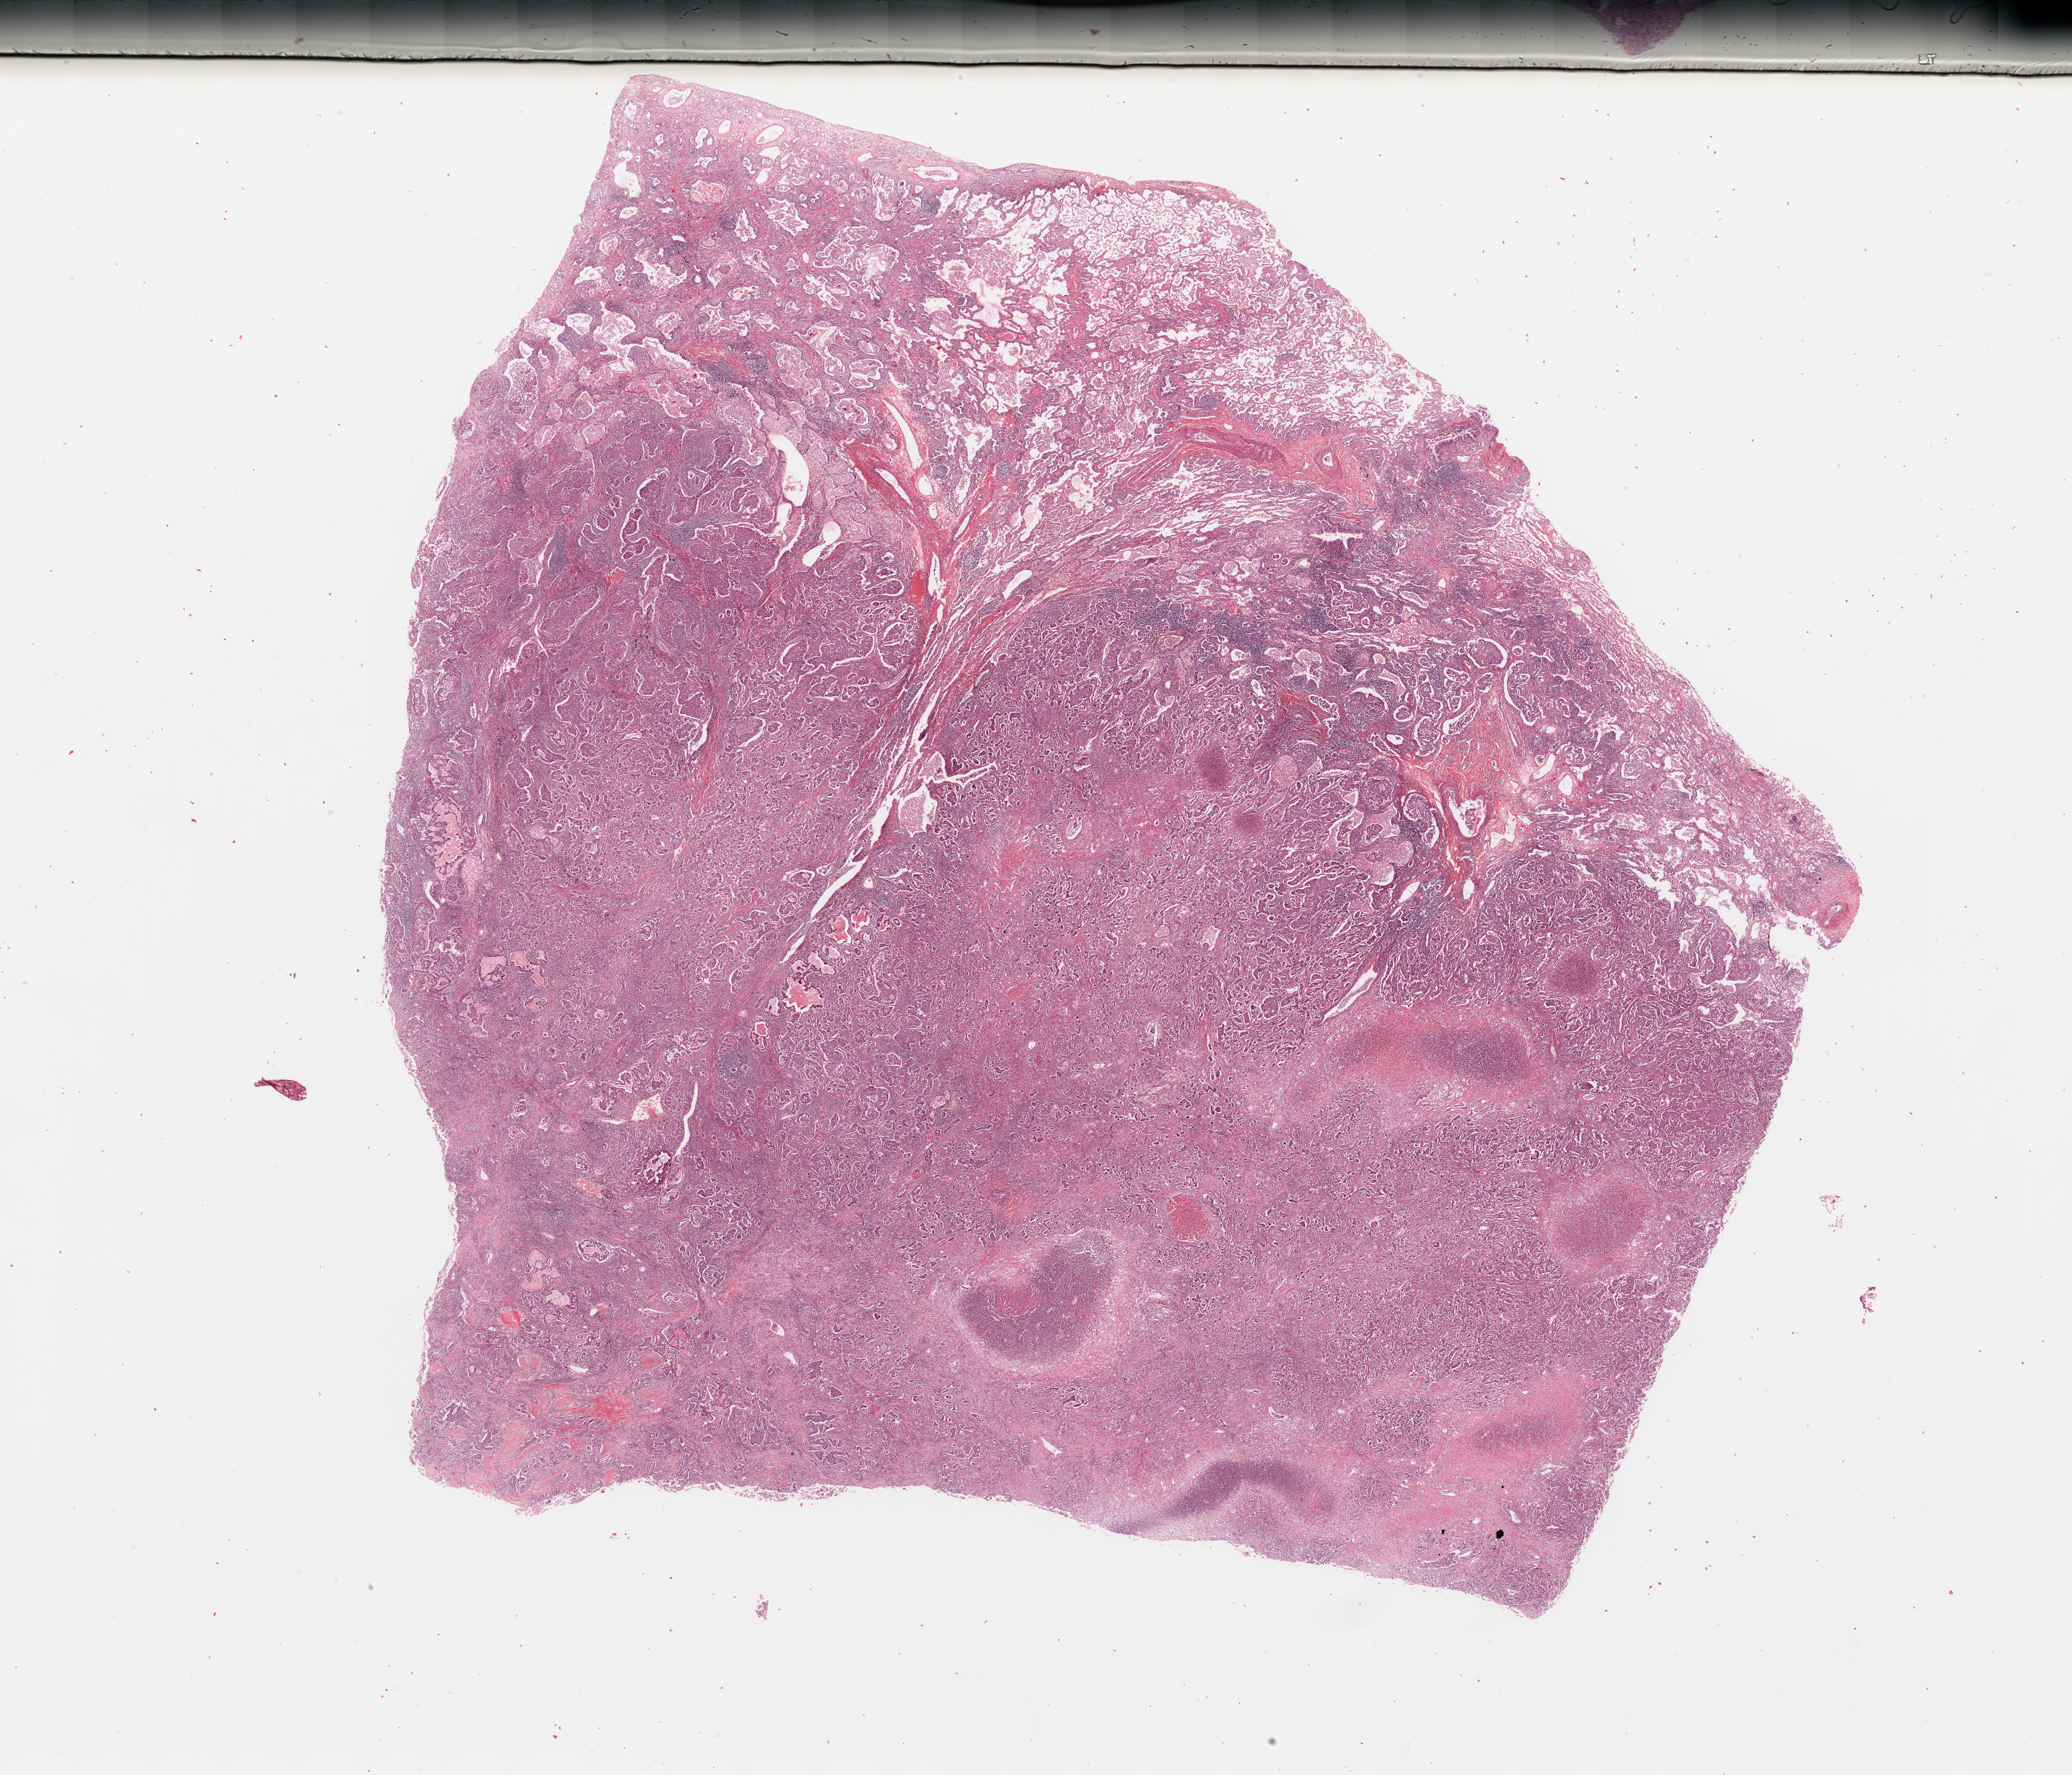
H&E-stained whole-slide image — whole scanned area (about 27.6 x 23.6 mm, acquisition: 20x scan) shown as a low-resolution overview. Lung, tumour tissue. Male, 49 y/o. Histologic grade: G3 (poorly differentiated).
AJCC pathologic stage: IIB. Diagnosis: Adenocarcinoma, NOS.